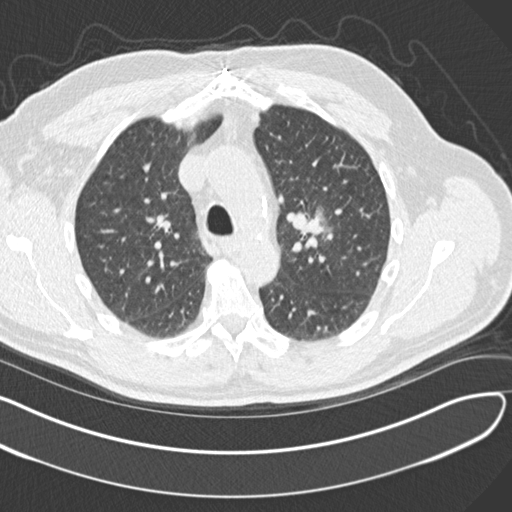
Low-dose screening chest CT, axial slice; second screening round (one year after baseline); lung window (W 1500 / L -600 HU); slice 45 of 164 in the series; 512 × 512 image matrix, field of view 372 × 372 mm. Male participant, aged 65 years at enrolment. Former smoker at enrolment.
• Expert reader's lesion annotation, bounding box <285,197,342,259> (left, top, right, bottom; pixels).
• The screening reader recorded 4 non-calcified nodules or masses ≥4 mm on this exam; which of them this box marks is not recorded.
• Later outcome: lung cancer diagnosed 577 days after this screen — acinar cell carcinoma, left upper lobe, stage IA (AJCC 6th edition), 25 mm at pathology.